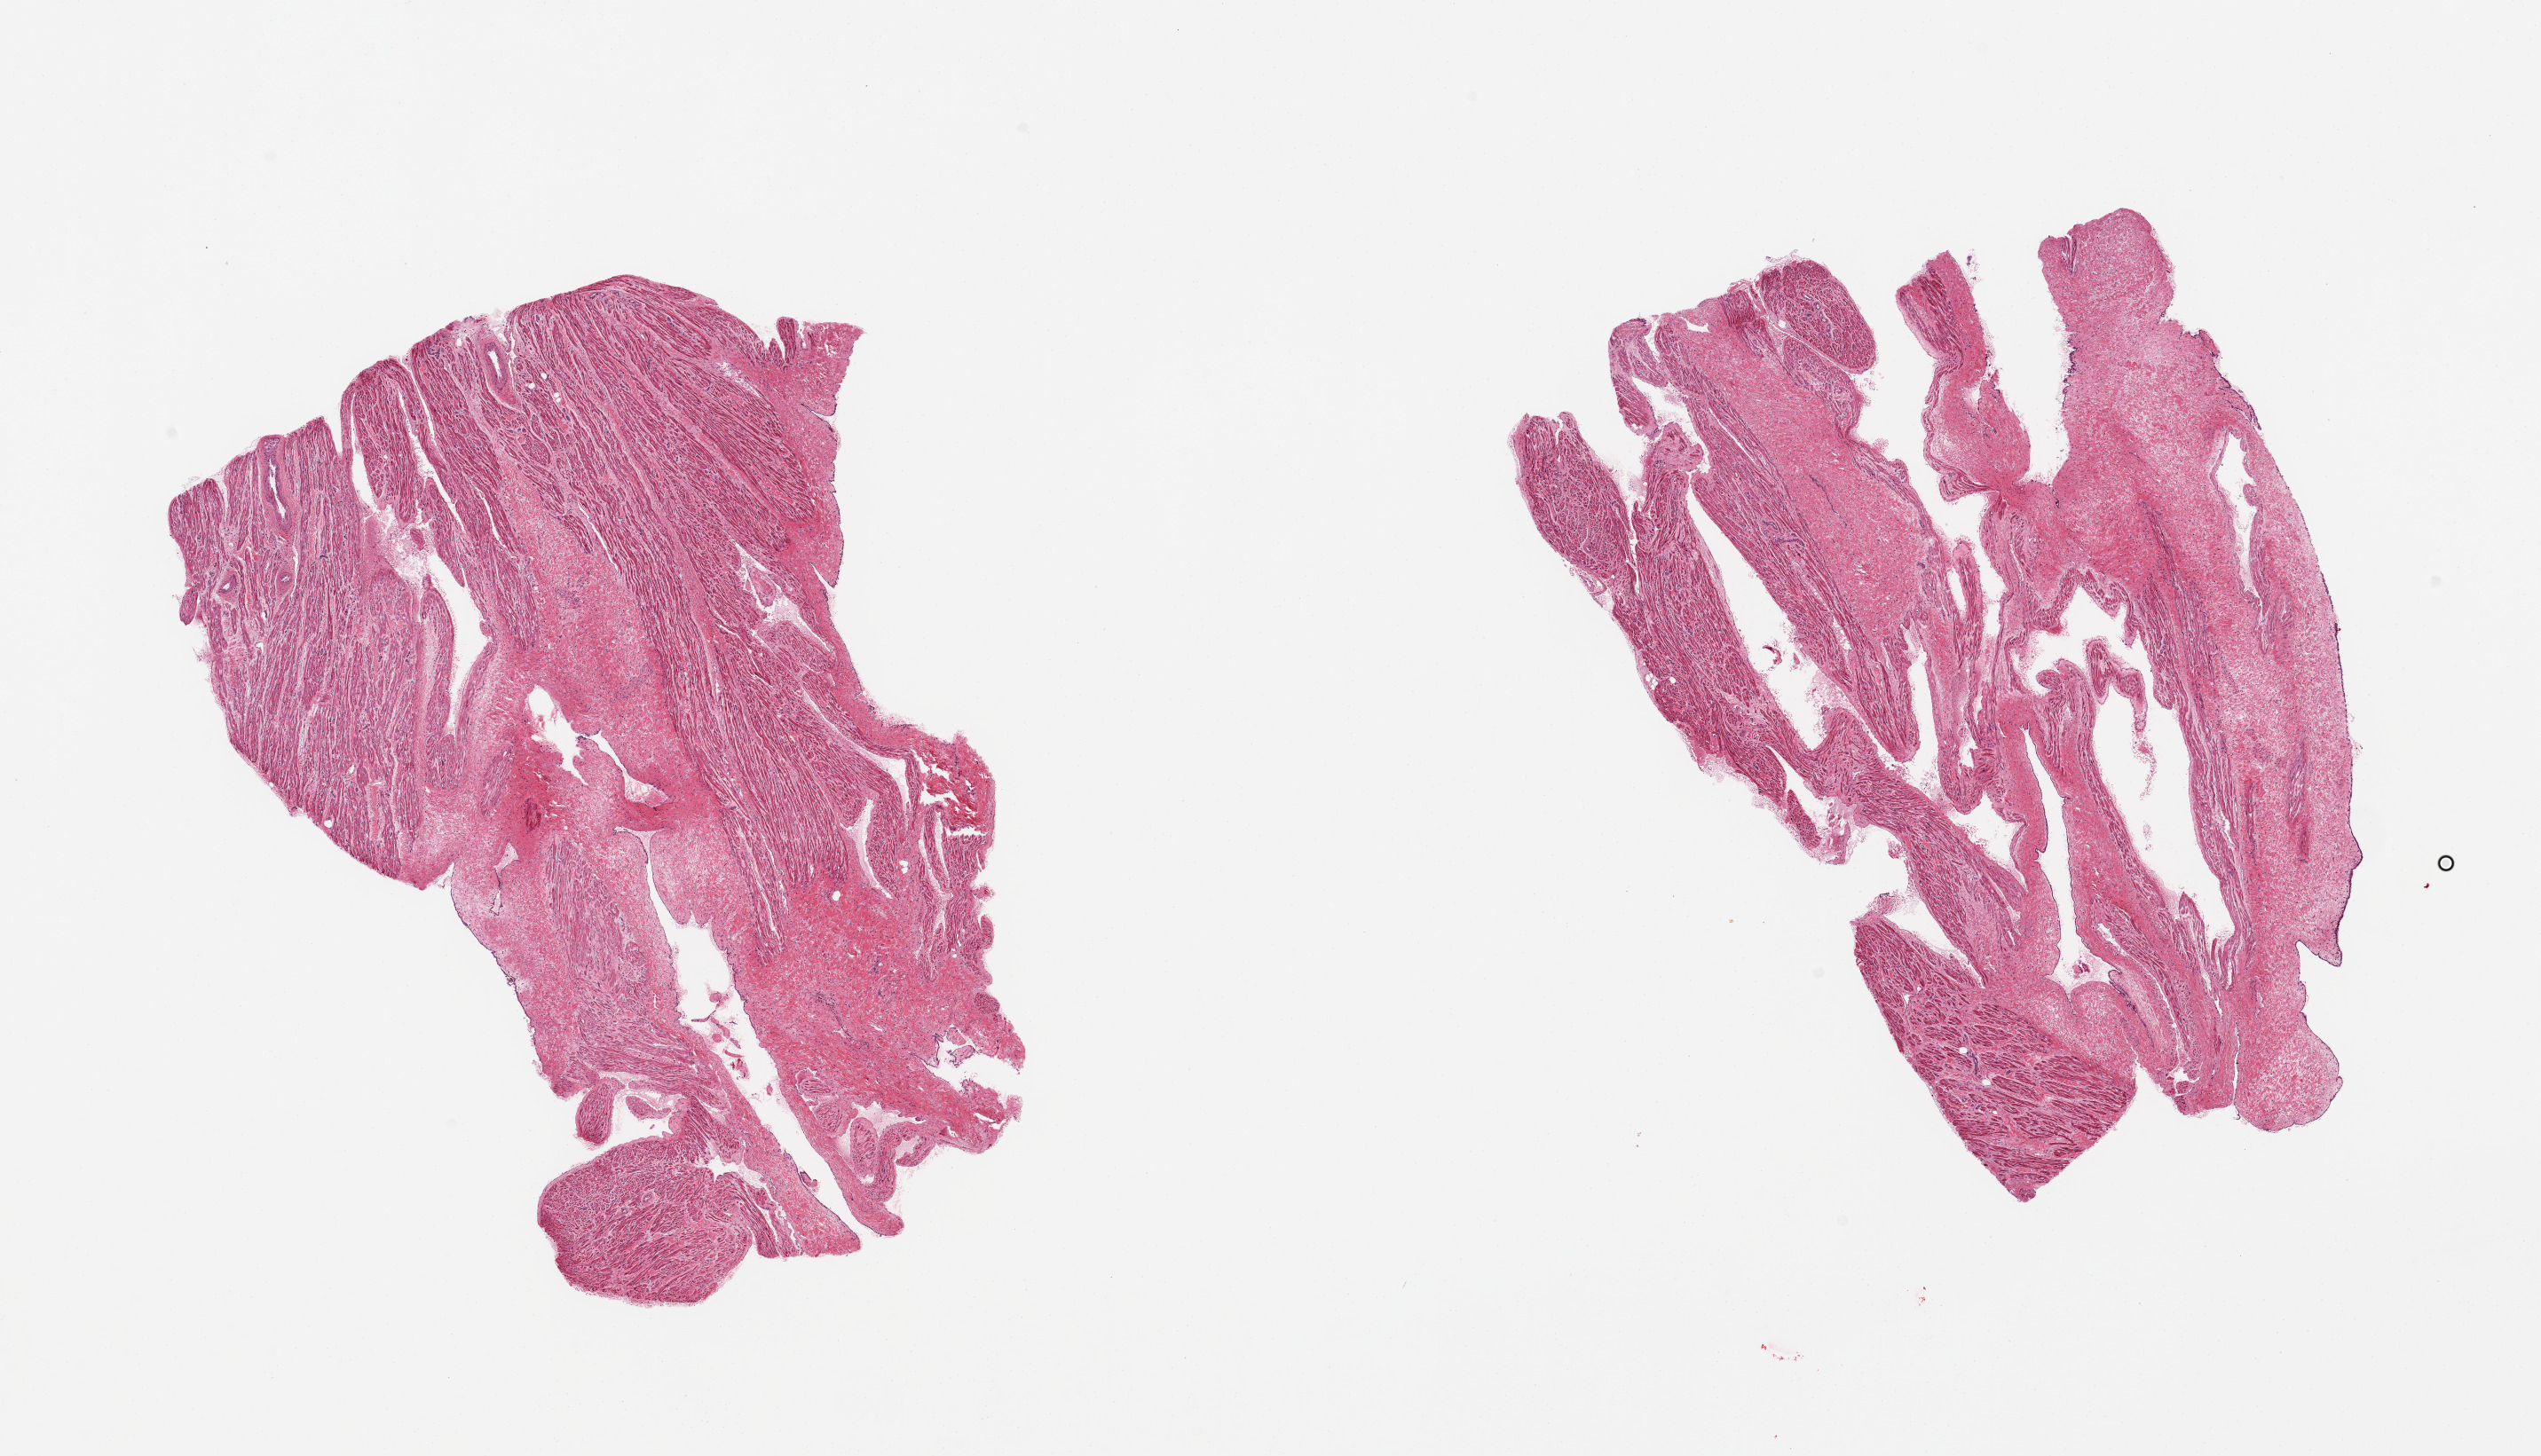
Digitized haematoxylin and eosin-stained section, brightfield, whole scanned area (about 22.6 x 13.0 mm, slide scanned at 20x) shown as a low-resolution overview; PAXgene-fixed, paraffin-embedded tissue; target tissue: auricular appendage; tissue donor sample. Donor sex: female.
Reviewer comment on this tissue sample: 2 pieces; 50% fibrous content.